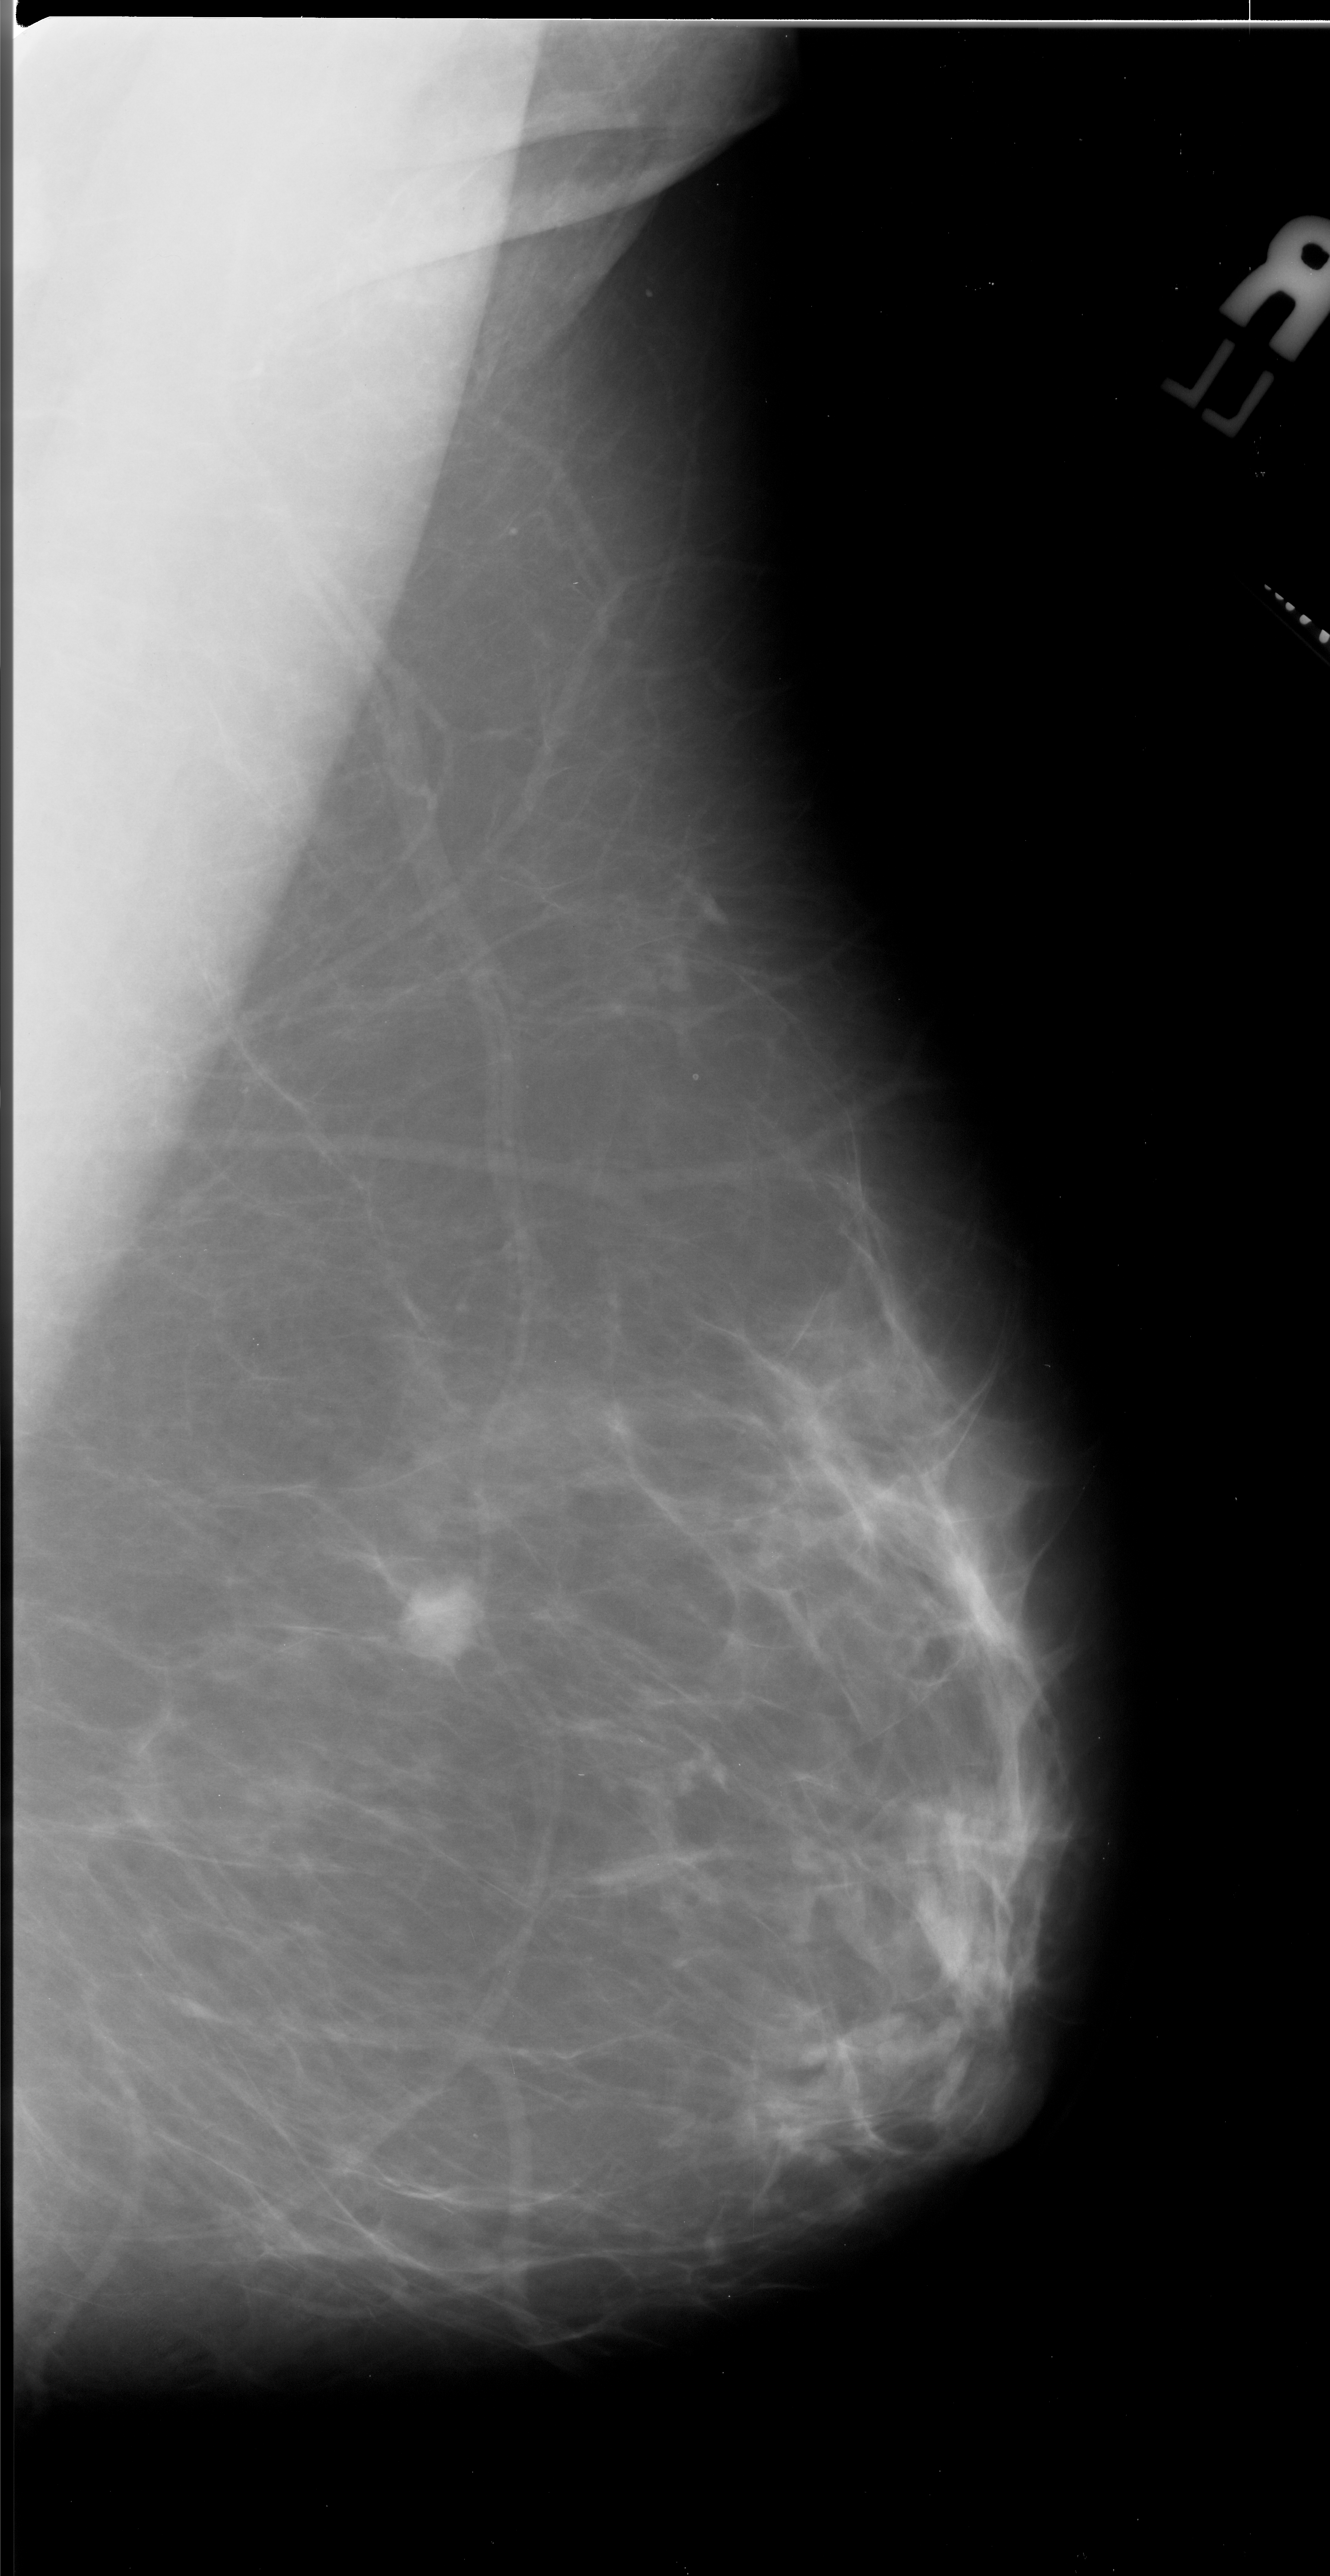
Scanned film-screen mammogram, right breast, mediolateral oblique (MLO) view, BI-RADS breast density category 2 (scale 1–4).
Mass, shape round, margins ill defined; BI-RADS assessment category 4; pathology result (as recorded, not read from the image): malignant.